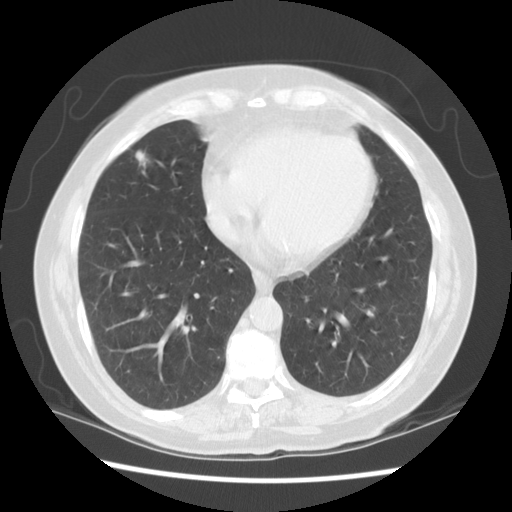
Low-dose screening chest CT, one axial slice. Slice 44 of 115 in the series (ordered by position). Lung window (W 1500 / L -600 HU). 512 × 512 image matrix, field of view 340 × 340 mm.
Outlined on this slice (manually delineated by an expert):
- lesion 1 (tumor, middle lobe of right lung): bounding box (x1, y1, x2, y2) in pixels: (135, 151, 148, 167)